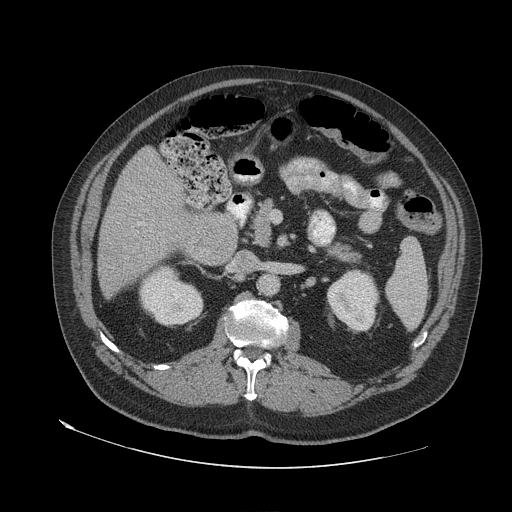
Contrast-enhanced abdominal CT (liver protocol), one axial slice. Slice 23 of 79 in the series (ordered by position). Reconstruction kernel STANDARD. 140 kVp. Soft-tissue window (W 400 / L 40 HU). 2.5 mm slice thickness. 512 × 512 image matrix. From the clinical record (not read from this slice): diagnosis: hepatocellular carcinoma (patient treated with transarterial chemoembolisation; whether this scan precedes or follows treatment is not stated here); TNM stage (as recorded): Stage-IVA; Child-Pugh class: A; tumour differentiation: well differentiated; tumour nodularity: multinodular.
Structures marked on this image (semi-automatic segmentation, software-assisted and operator-edited):
- liver parenchyma outside the tumour (the mass and vessels are separate outlines, so this box may not span the whole liver): box from (x=98, y=146) to (x=216, y=298) px
- liver vessels: (x=138, y=223)–(x=140, y=225)